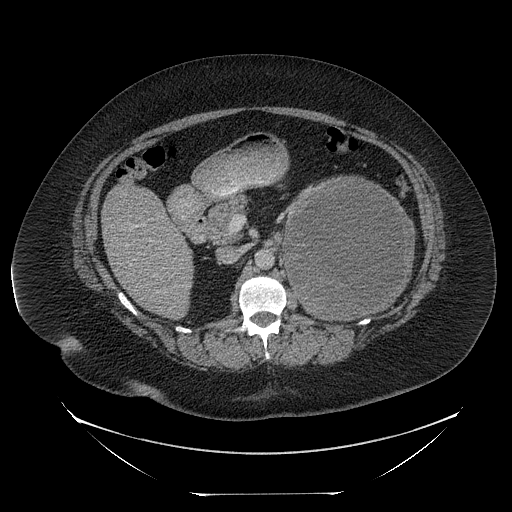
Contrast-enhanced abdominal CT, one axial slice. Position 134 of 205 along the scan axis. Reconstruction kernel STANDARD. Intravenous contrast given. Soft-tissue window (W 400 / L 40 HU). 2.5 mm slice thickness. 512 × 512 image matrix, field of view 500 × 500 mm. Patient: female, 53 years. From the clinical record (not read from this slice): diagnosis: adrenocortical carcinoma; tumour side: left adrenal; tumour size at pathology: 17 cm; Ki-67 index: 20 %; stage (as recorded): 3.
Annotated regions visible in this slice (semi-automatic segmentation, software-assisted and operator-edited):
- mass: bounding box (x1, y1, x2, y2) in pixels: (284, 179, 412, 320)